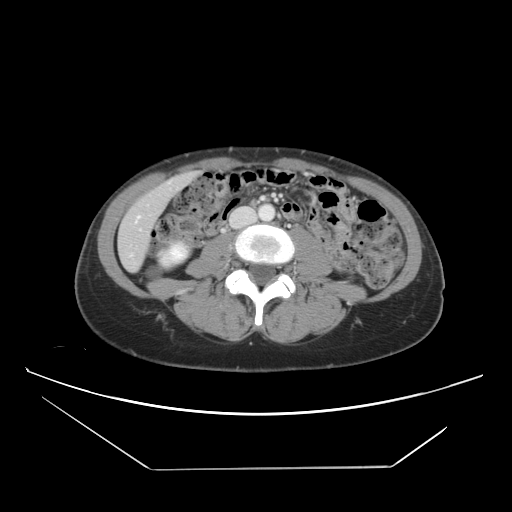
Contrast-enhanced abdominal CT, one axial slice; slice 10 of 42 in the series (ordered by position); 120 kVp; intravenous contrast given; soft-tissue window (W 400 / L 40 HU); 5 mm slice thickness; 512 × 512 image matrix, field of view 399 × 399 mm. Female patient, age 52 years. Case-level facts recorded for this patient, not image findings: diagnosis: colorectal cancer liver metastases, imaged before liver resection; multiple liver metastases: yes; largest metastasis: 5.5 cm; chemotherapy before resection: yes.
Structures marked on this image (outlined manually by an expert reader):
- hepatic veins: box from (x=134, y=180) to (x=178, y=225) px
- liver: (x=120, y=174)–(x=193, y=269)
- planned liver remnant (the part of the liver to remain after resection): (x=130, y=174)–(x=193, y=221)
- portal vein (with intrahepatic branches): (x=261, y=197)–(x=264, y=200)